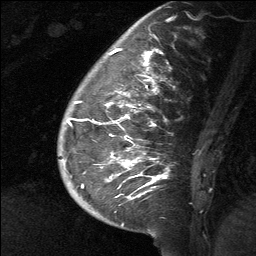
Breast MRI (dynamic contrast-enhanced), one sagittal slice. Position 20 of 64 along the scan axis. Dynamic contrast-enhanced study with each time point stored as its own series, time point 2 of 3 at this slice position (early post-contrast, ordered by acquisition time). 1.5 T. TE 4.8 ms, TR 27 ms. 2 mm slice thickness. 256 × 256 image matrix, field of view 180 × 180 mm. Female patient, age 39 years. Case-level facts recorded for this patient, not image findings: setting: breast cancer imaged before/during neoadjuvant chemotherapy; receptor status: HER2-positive.
Outlined on this slice (semi-automatically segmented with operator editing):
- analysis volume of interest (the breast-tissue region the enhancement analysis was run in; not a lesion): box from (x=58, y=40) to (x=201, y=217) px
- tumour enhancement mask (voxels above the 90 % enhancement threshold inside the analysis volume of interest): (x=68, y=49)–(x=164, y=200)